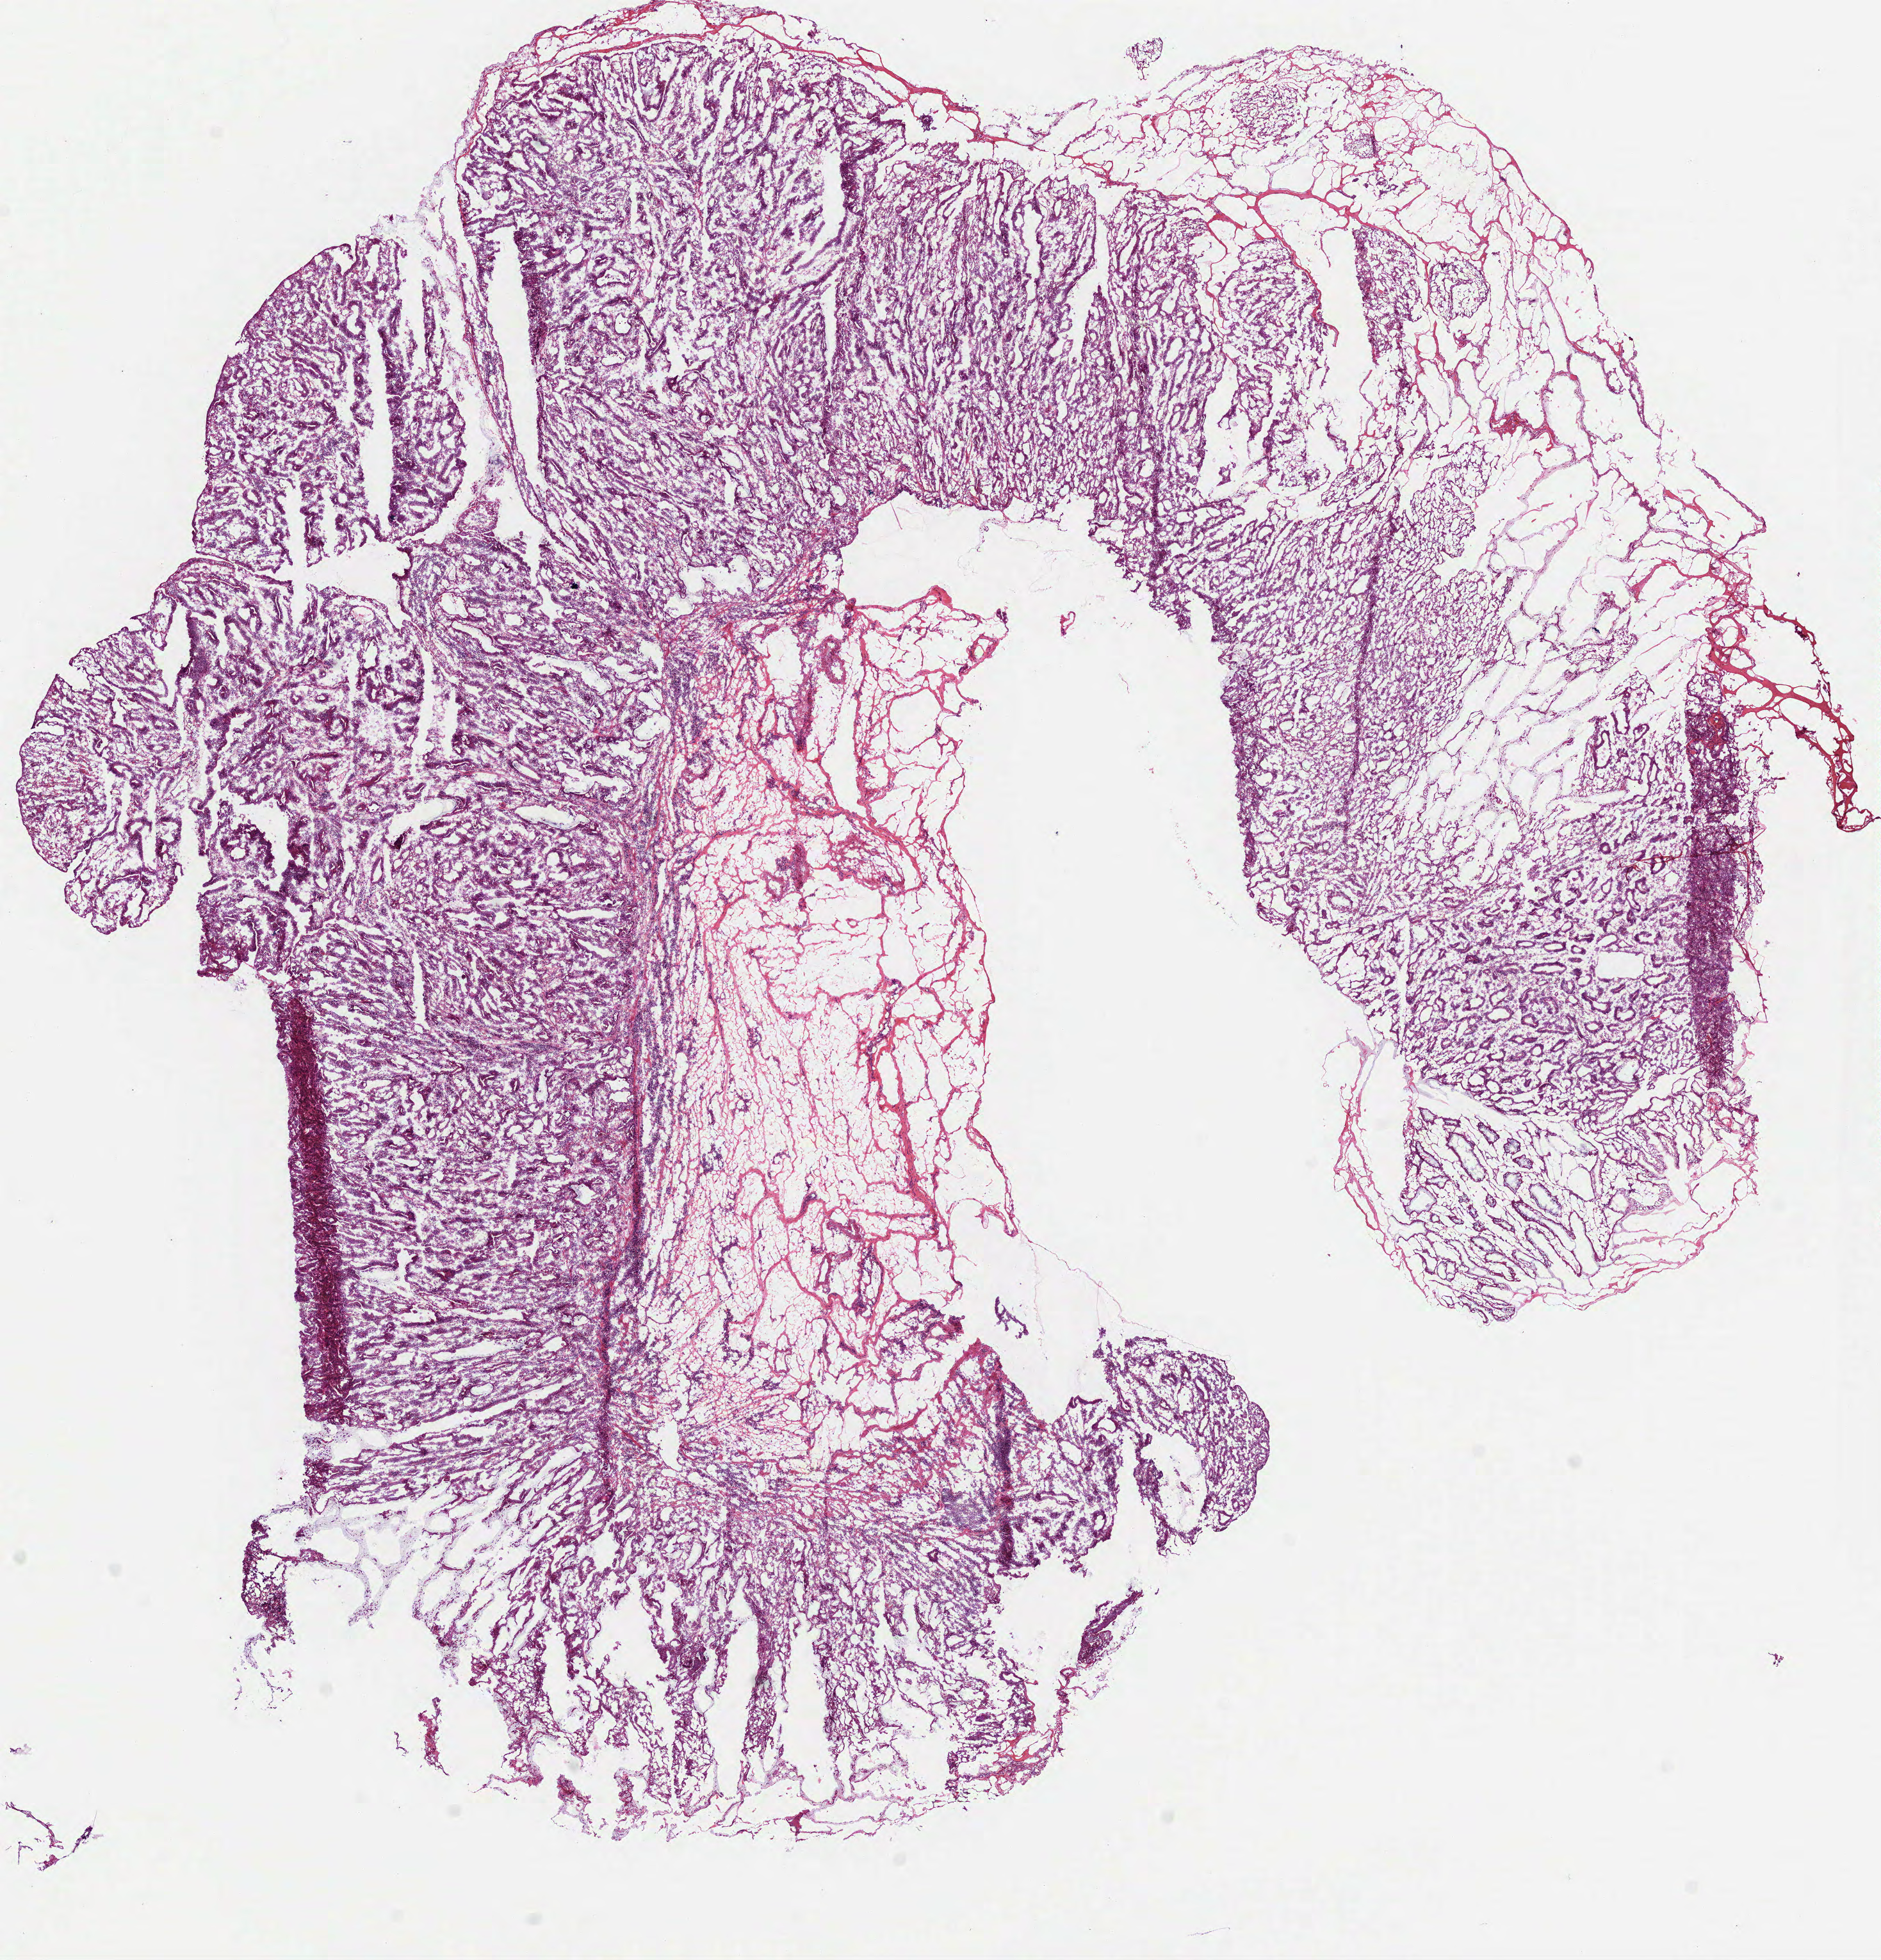
H&E whole-slide image — a low-resolution overview of the entire scanned area, about 11.8 x 12.3 mm (acquisition: 40x scan). Frozen section from the top of the tissue portion. Primary tumour sample from the stomach. Male, age 81 years at initial diagnosis. Histologic grade: G2 (moderately differentiated). Composition of this section per pathologist review: tumour cells 80%, tumour nuclei 70%, normal cells 5%, stromal cells 15%, necrosis 0%. Inflammatory infiltration, as recorded: lymphocyte infiltration 15%.
AJCC pathologic stage: IA (7th edition). Lymph nodes positive (case pathology): 0 of 4 examined. Histologic diagnosis: Papillary adenocarcinoma, NOS (body of stomach).